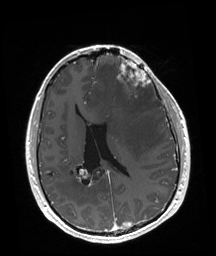
Brain MRI from a brain-tumour surgery series, one axial slice; position 77 of 192 along the scan axis; T1-weighted post-contrast; 1 mm slice thickness; 216 × 256 image matrix. Case-level facts recorded for this patient, not image findings: tumour location: Left Frontal.
Annotated regions visible in this slice (manually delineated by an expert):
- tumour: bounding box [x1, y1, x2, y2] px = [117, 59, 150, 101]